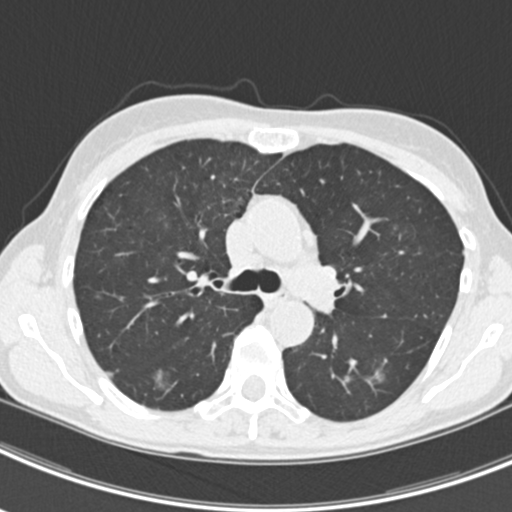
Low-dose screening chest CT, axial slice. Second screening round (one year after baseline). Lung window (W 1500 / L -600 HU). 2 mm slice thickness. Standard (soft-tissue) reconstruction kernel (B30f). 512 × 512 image matrix. Female participant, aged 63 years at enrolment. Current smoker at enrolment.
- 2 expert-annotated lung lesions on this slice (largest first), box from (x=365, y=361) to (x=401, y=393) px; (x=143, y=364)–(x=177, y=397).
- The screening reader recorded 9 non-calcified nodules or masses ≥4 mm on this exam (left upper lobe, right upper lobe, left upper lobe, left lower lobe, right middle lobe, left lower lobe, left lower lobe, right lower lobe, right lower lobe); which of them these boxes mark is not recorded.
- Official screen result: positive, other.
- Lung cancer was diagnosed 408 days after this screen (after the third annual screen): bronchiolo-alveolar adenocarcinoma, NOS, right upper lobe, right middle lobe, right lower lobe, left upper lobe, left lower lobe, moderately differentiated (G2), stage IV (AJCC 6th edition).